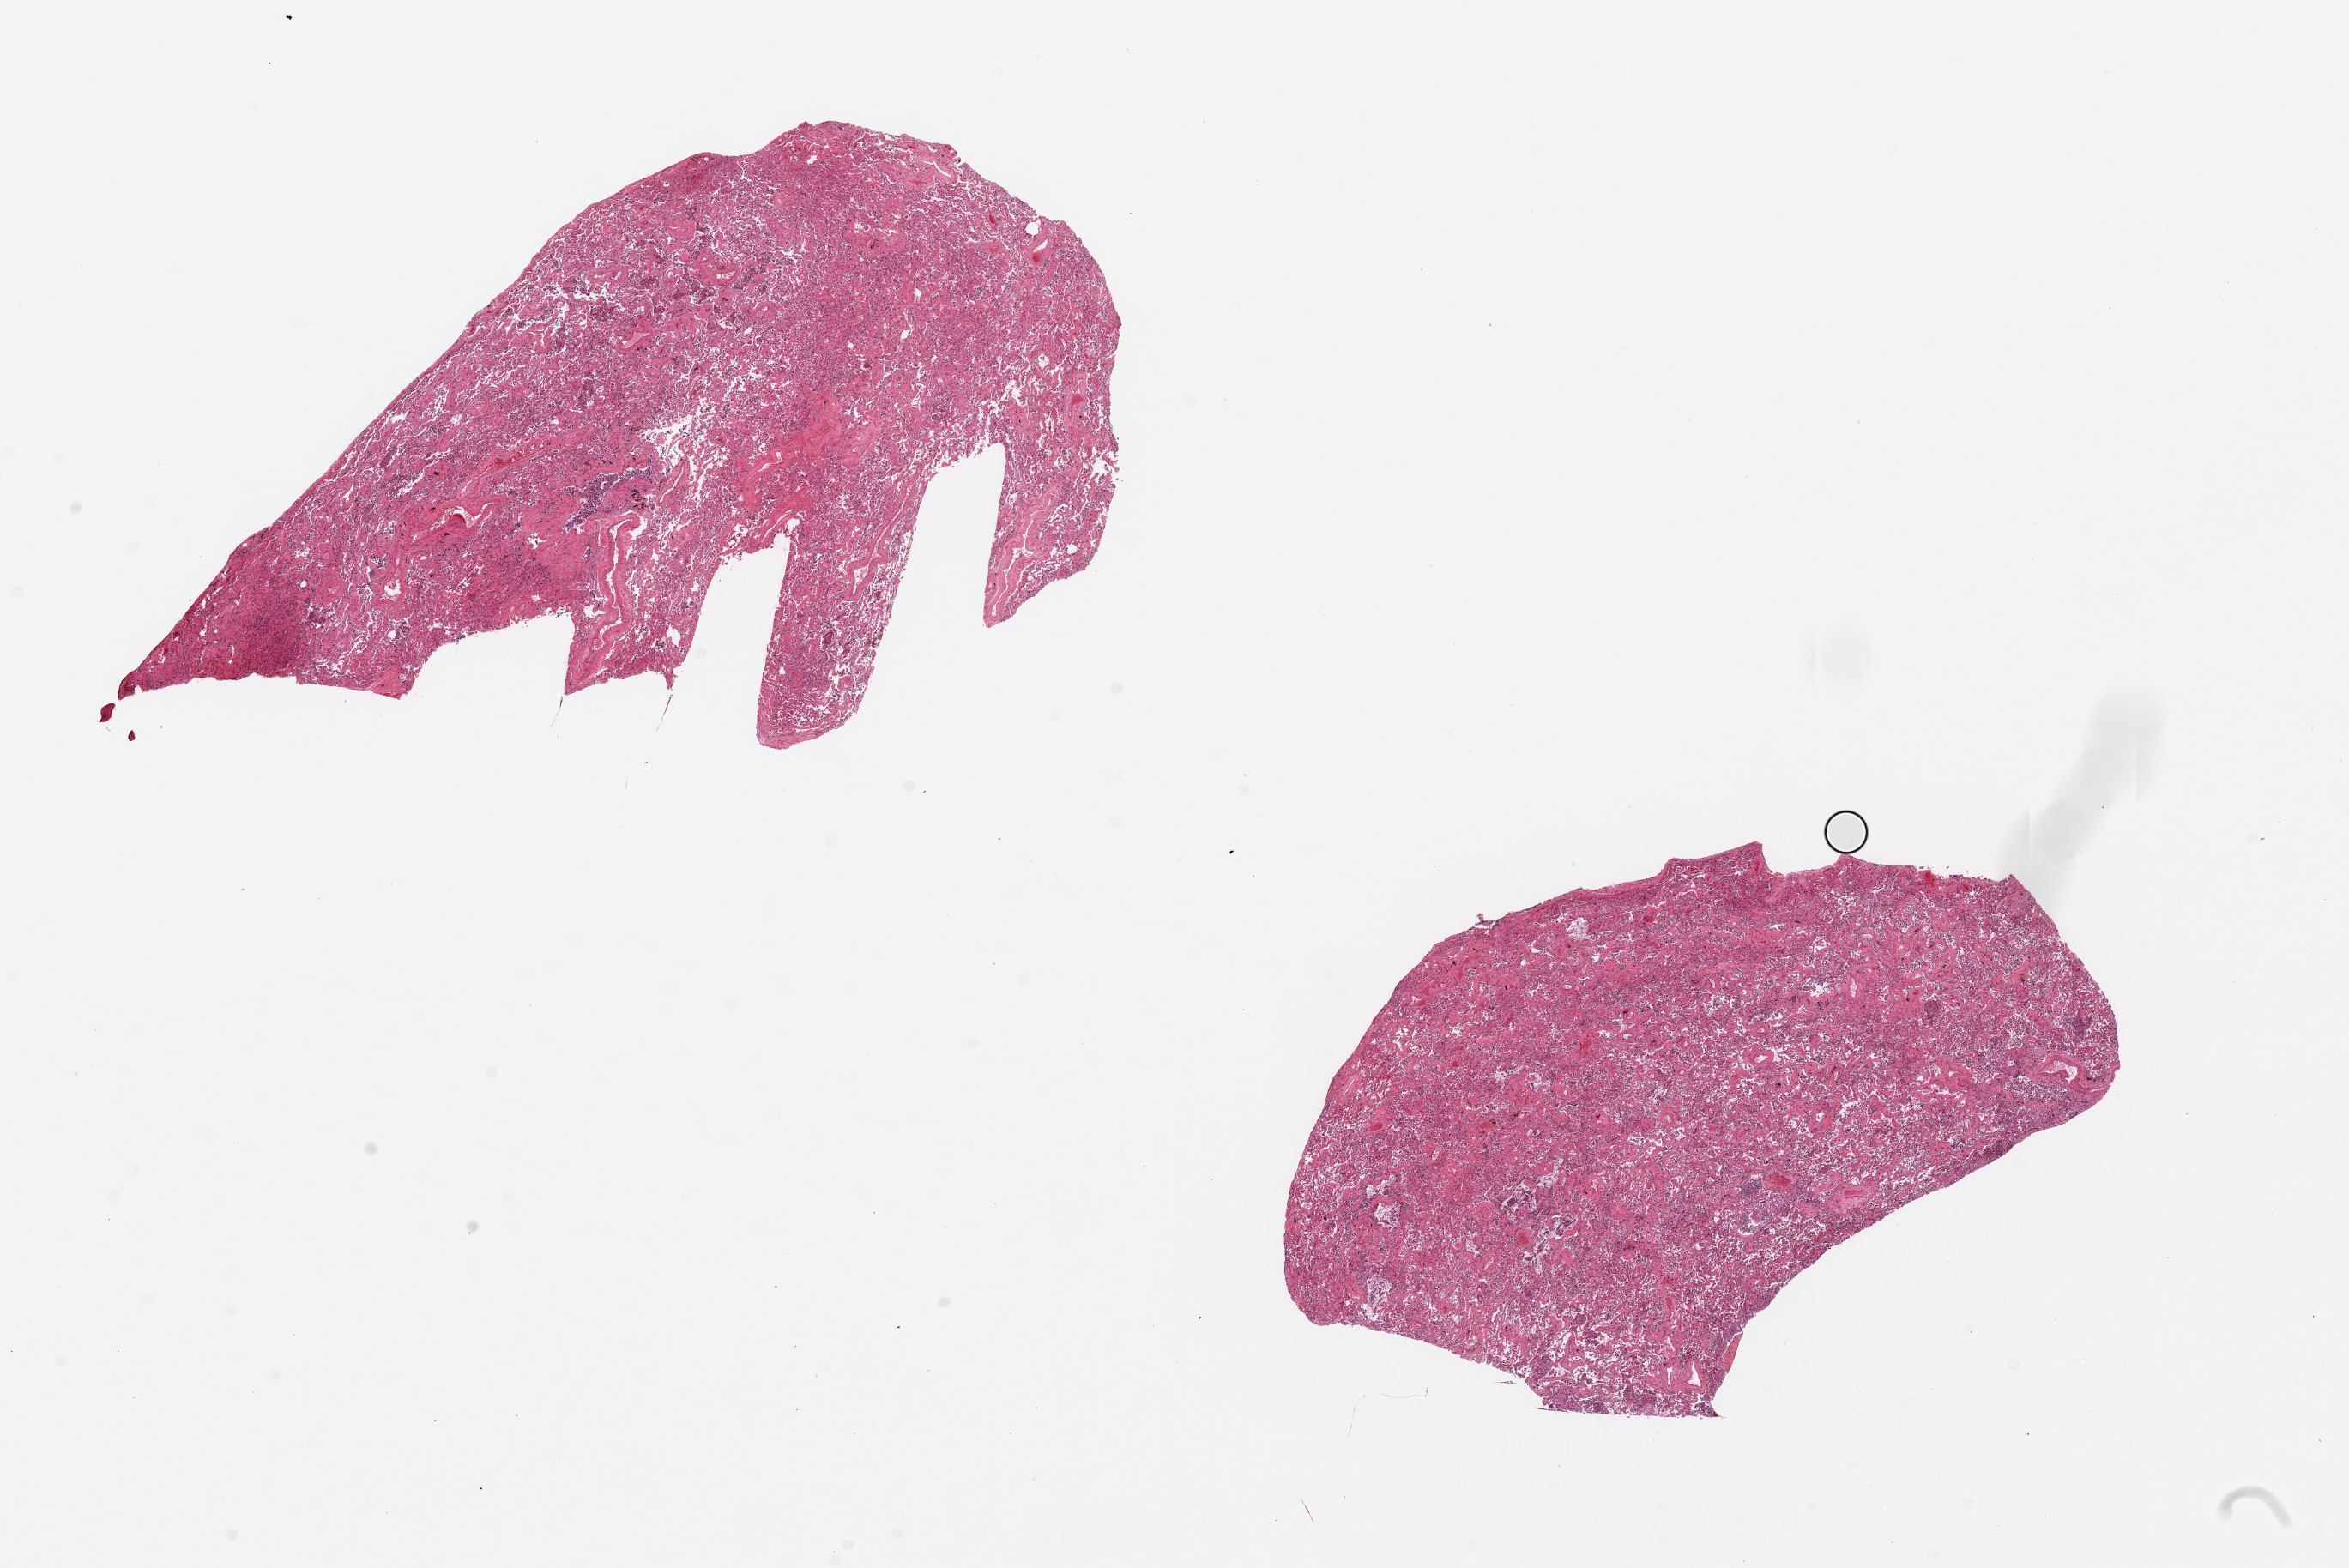
Digitized H&E-stained section, low-resolution overview of the scanned area, about 21.7 x 14.5 mm; PAXgene-fixed paraffin-embedded (PFPE) section; target tissue: lung; tissue donor sample. Donor: male.
Pathologist's review note for this sample: 2 pieces ~8x5mm; Diffuse interstitial fibrosis, ? diffuse alveolar damage sequence, micro foci of acute inflammation.